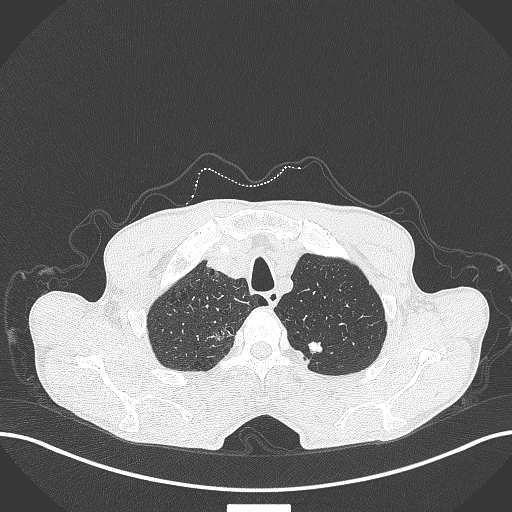
Chest CT, one axial slice. Position 378 of 445 along the scan axis. Reconstruction kernel B70f. Lung window (W 1500 / L -600 HU). 512 × 512 image matrix, field of view 400 × 400 mm. Male patient, age 70 years. Case-level facts recorded for this patient, not image findings: clinical TNM (as recorded): T1a N0 M0.
Structures marked on this image (rectangle marked by the reading radiologist):
- lung tumour (recorded histology: adenocarcinoma): bounding box [x1, y1, x2, y2] px = [209, 321, 236, 347]